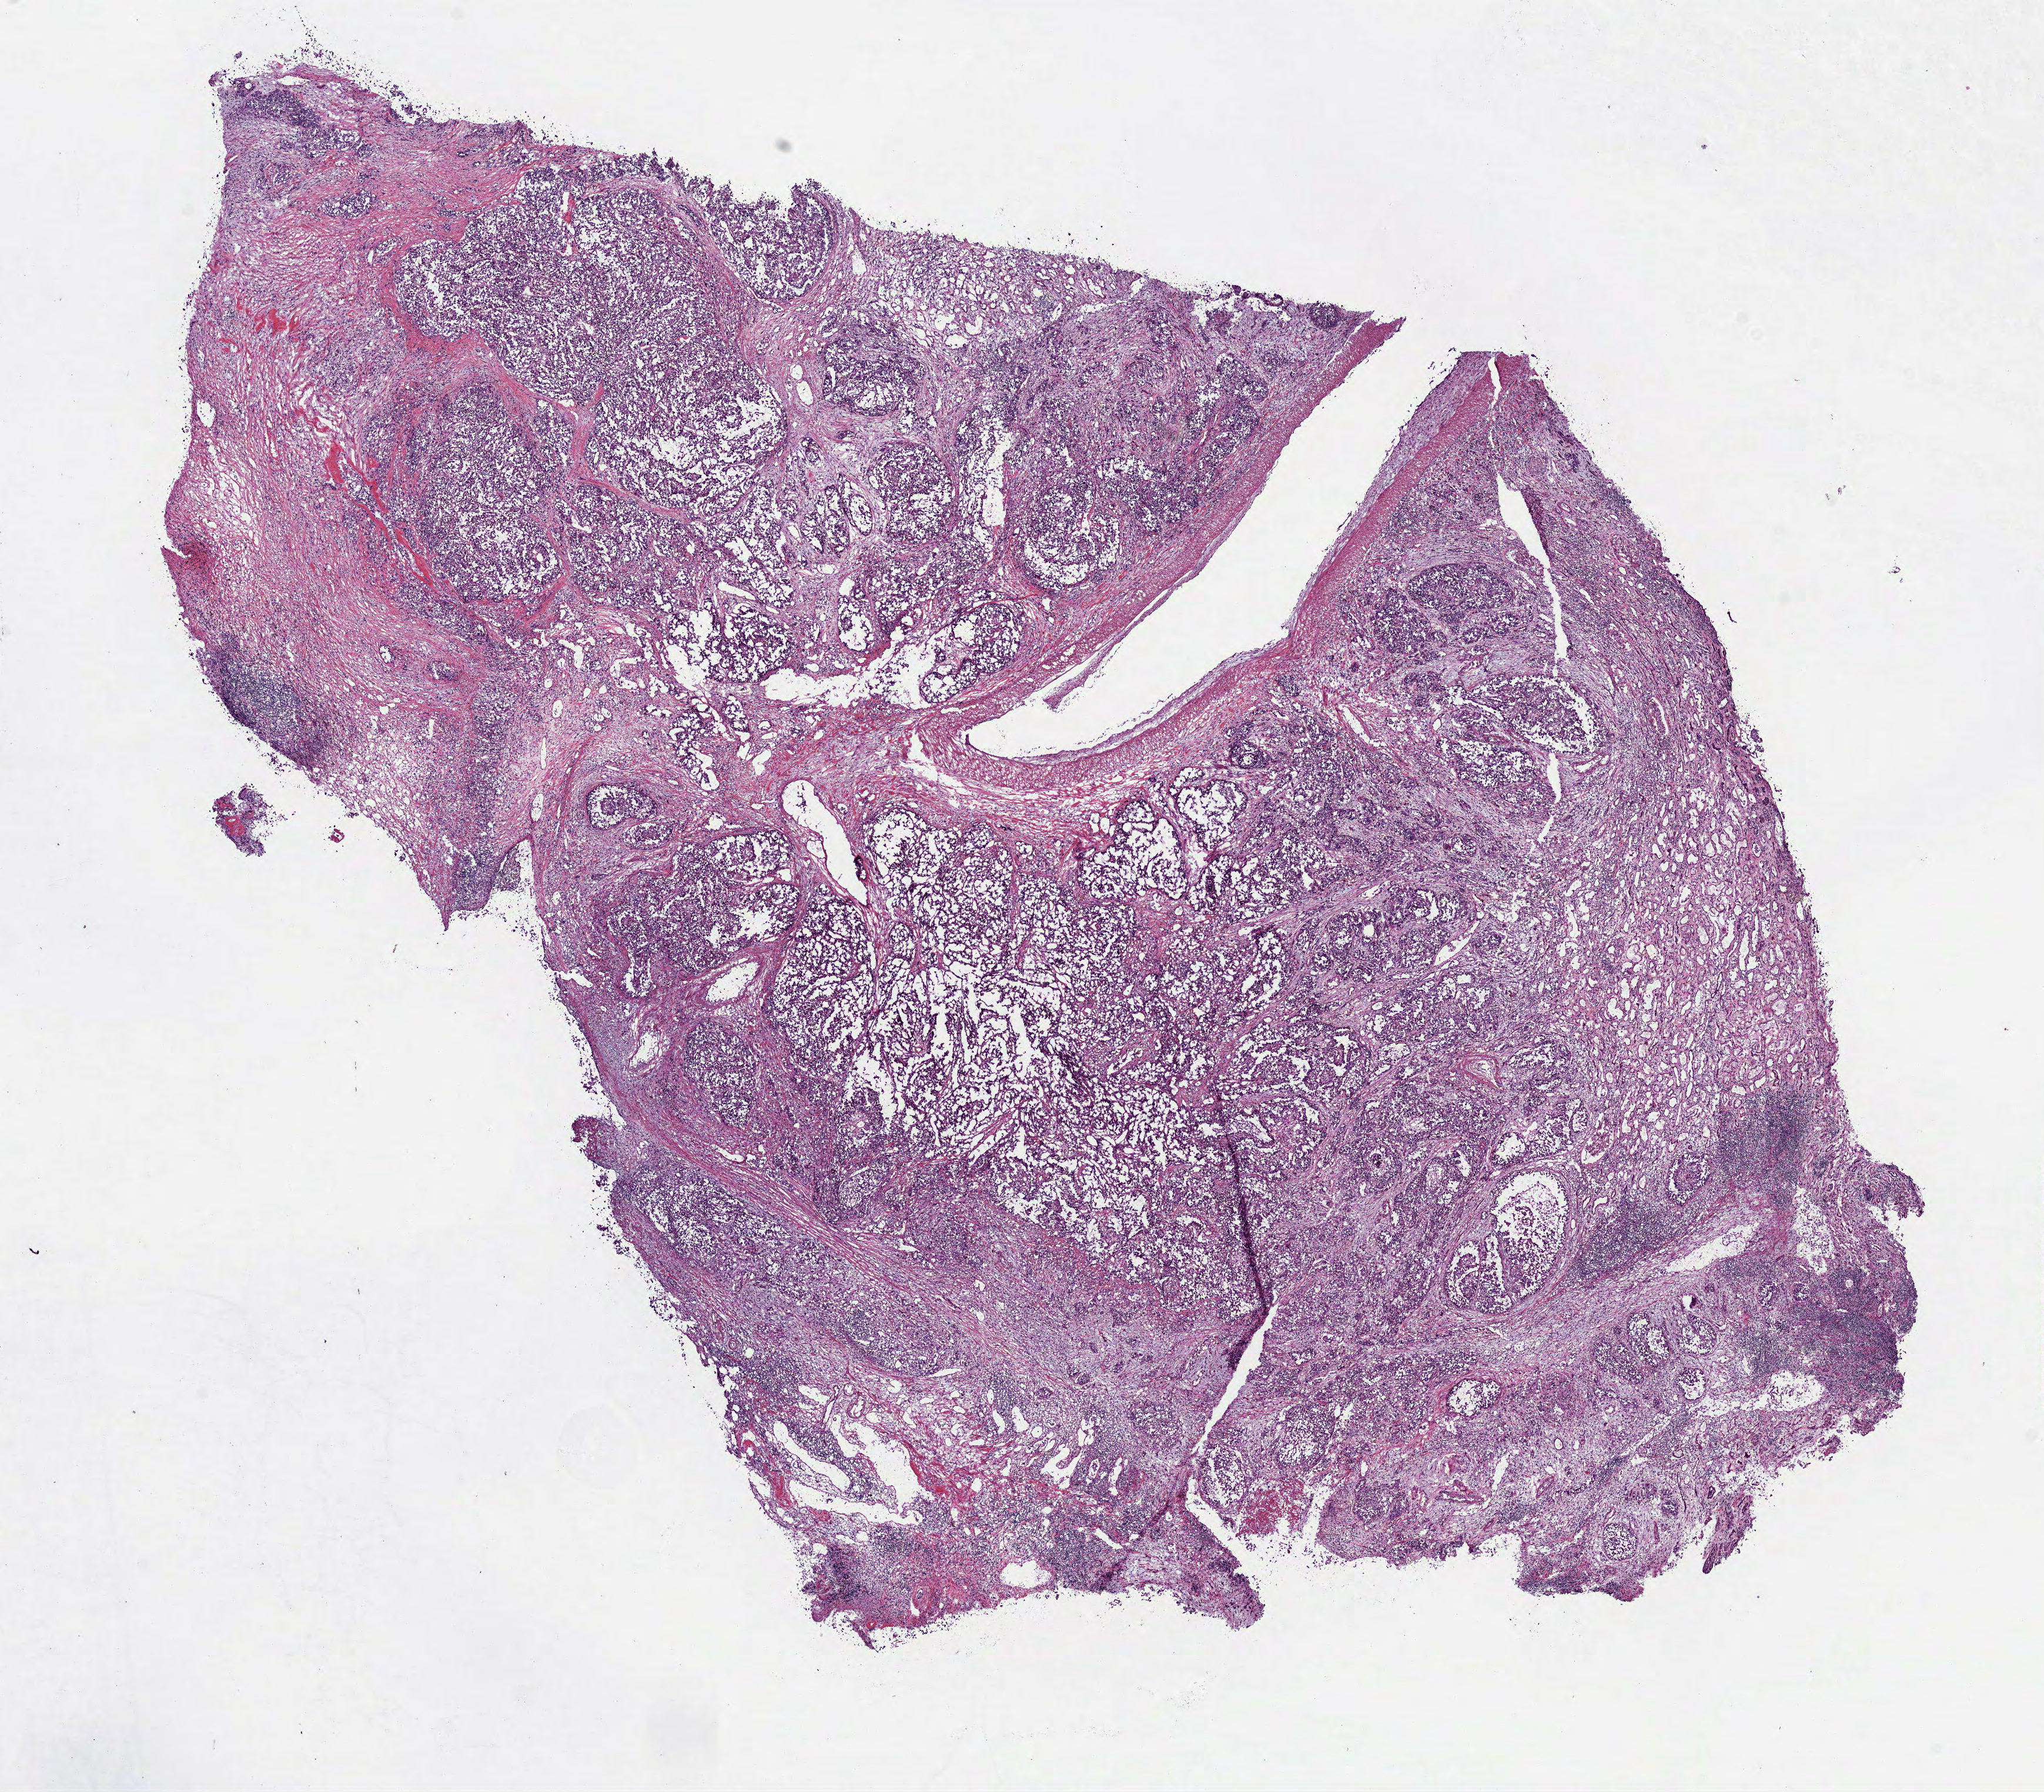
Whole-slide histology image, Hematoxylin and eosin (H&E) stained, a low-resolution overview of the entire scanned area, about 14.0 x 12.3 mm (from a 40x scan), frozen section, kidney, primary tumour sample. Patient: male, age at initial diagnosis 42 years. Pathologist review of this section (percent, as recorded): tumour cells 80%, tumour nuclei 75%, normal cells 0%, stromal cells 20%, necrosis 0%.
• diagnosis: Papillary adenocarcinoma, NOS
• laterality: left
• AJCC pathologic stage: IV
• TNM: T3b N1 M1